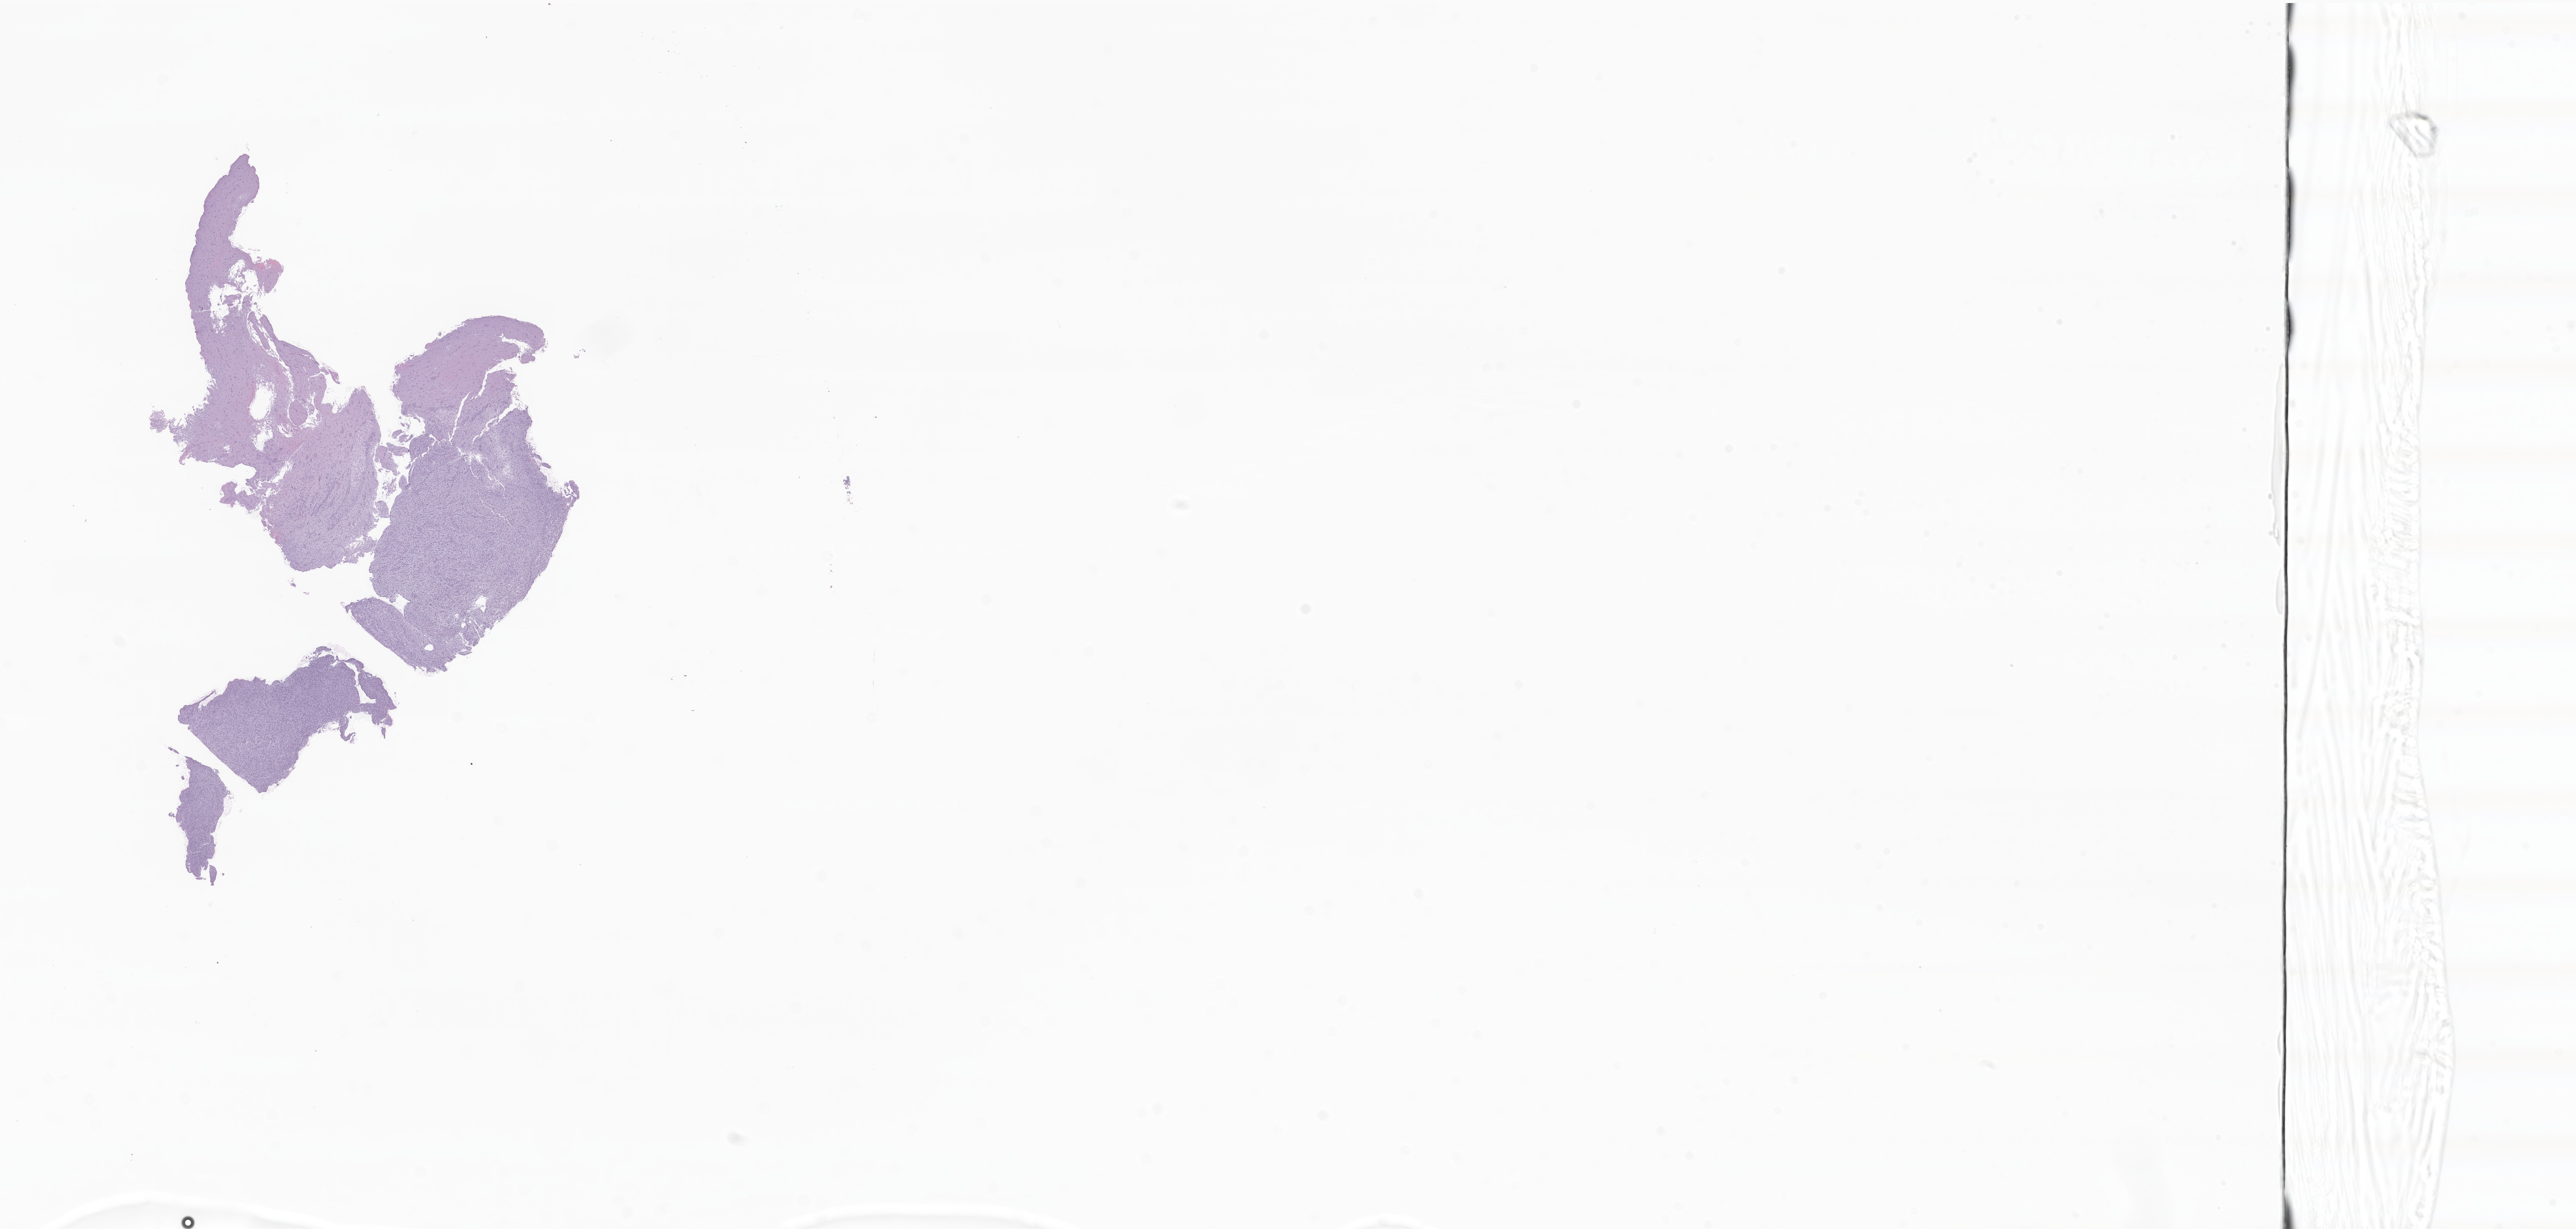
Digitized haematoxylin and eosin-stained section of tumor tissue from the brain — whole scanned area (about 31.9 x 15.2 mm) shown as a low-resolution overview; FFPE section. Female patient, age 39 months (3 years 3 months).
Diagnosis: Glioma, malignant.